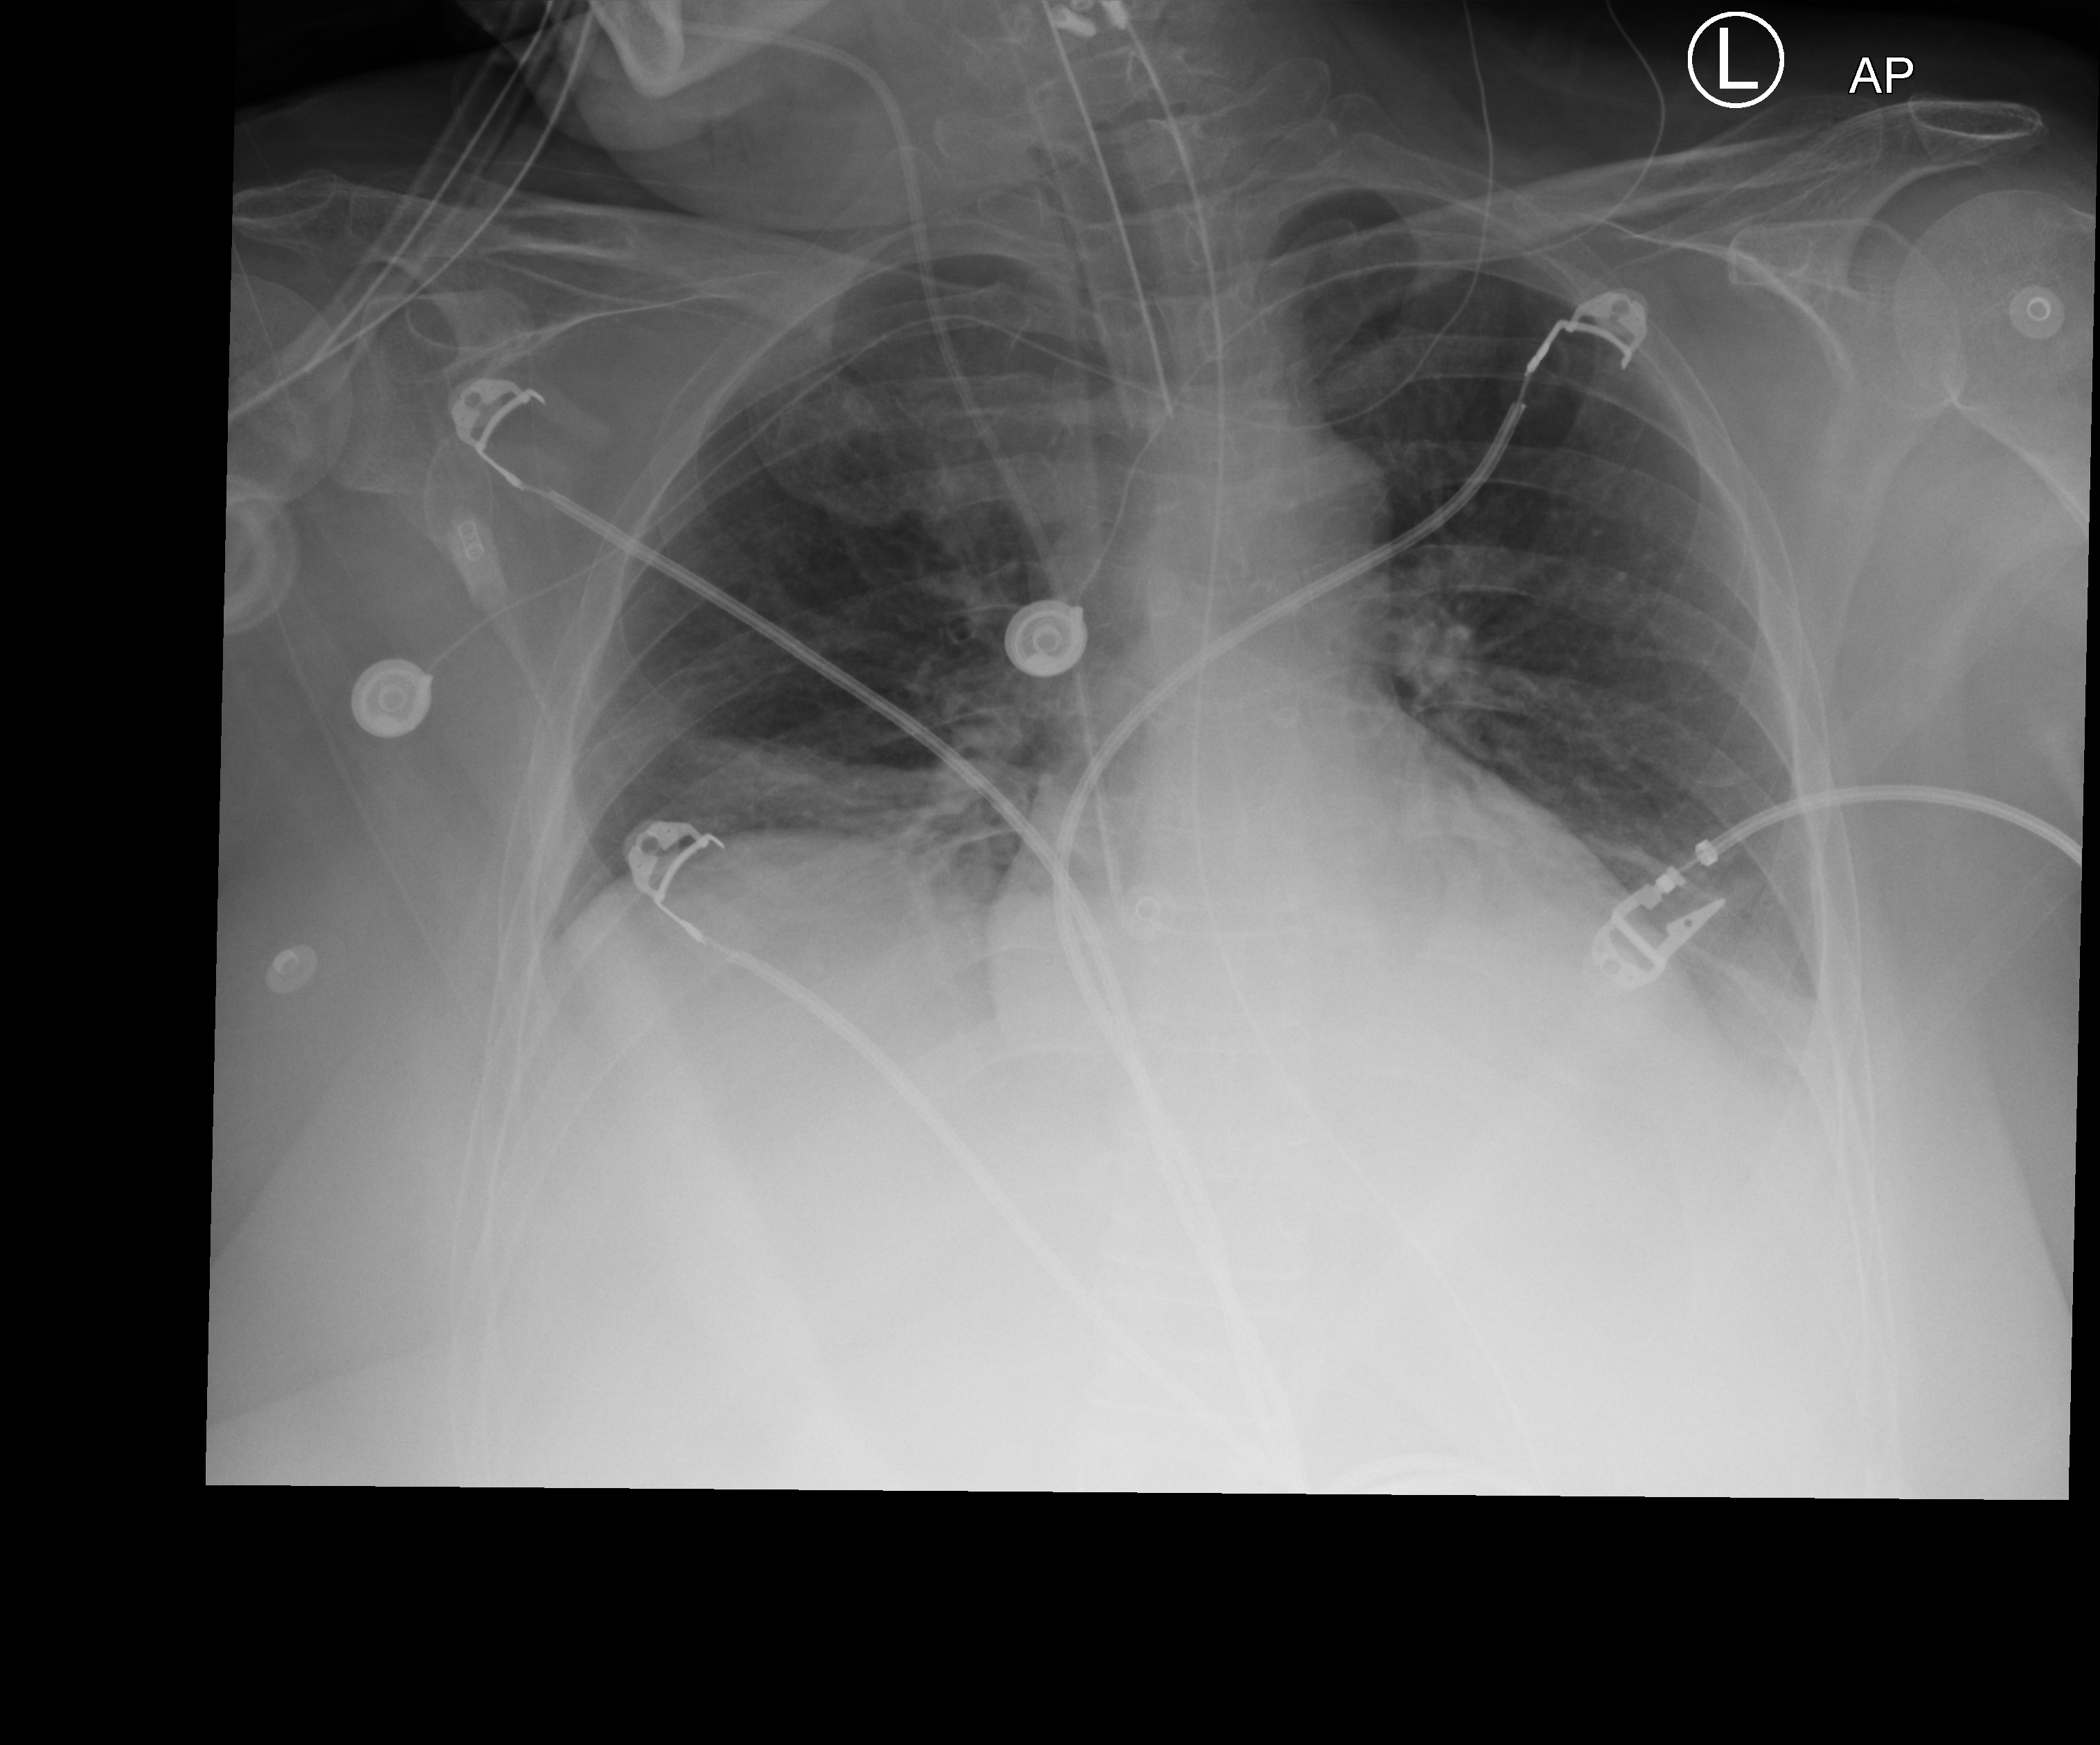
Bedside chest radiograph (computed radiography), anteroposterior (AP) projection. Patient hospitalised with COVID-19; female, aged 18–59 years.
From the hospital-stay record, not from the radiograph (when in the stay this image was taken is not recorded):
- mechanically ventilated during this hospital stay: no
- admitted to intensive care during this hospital stay: yes